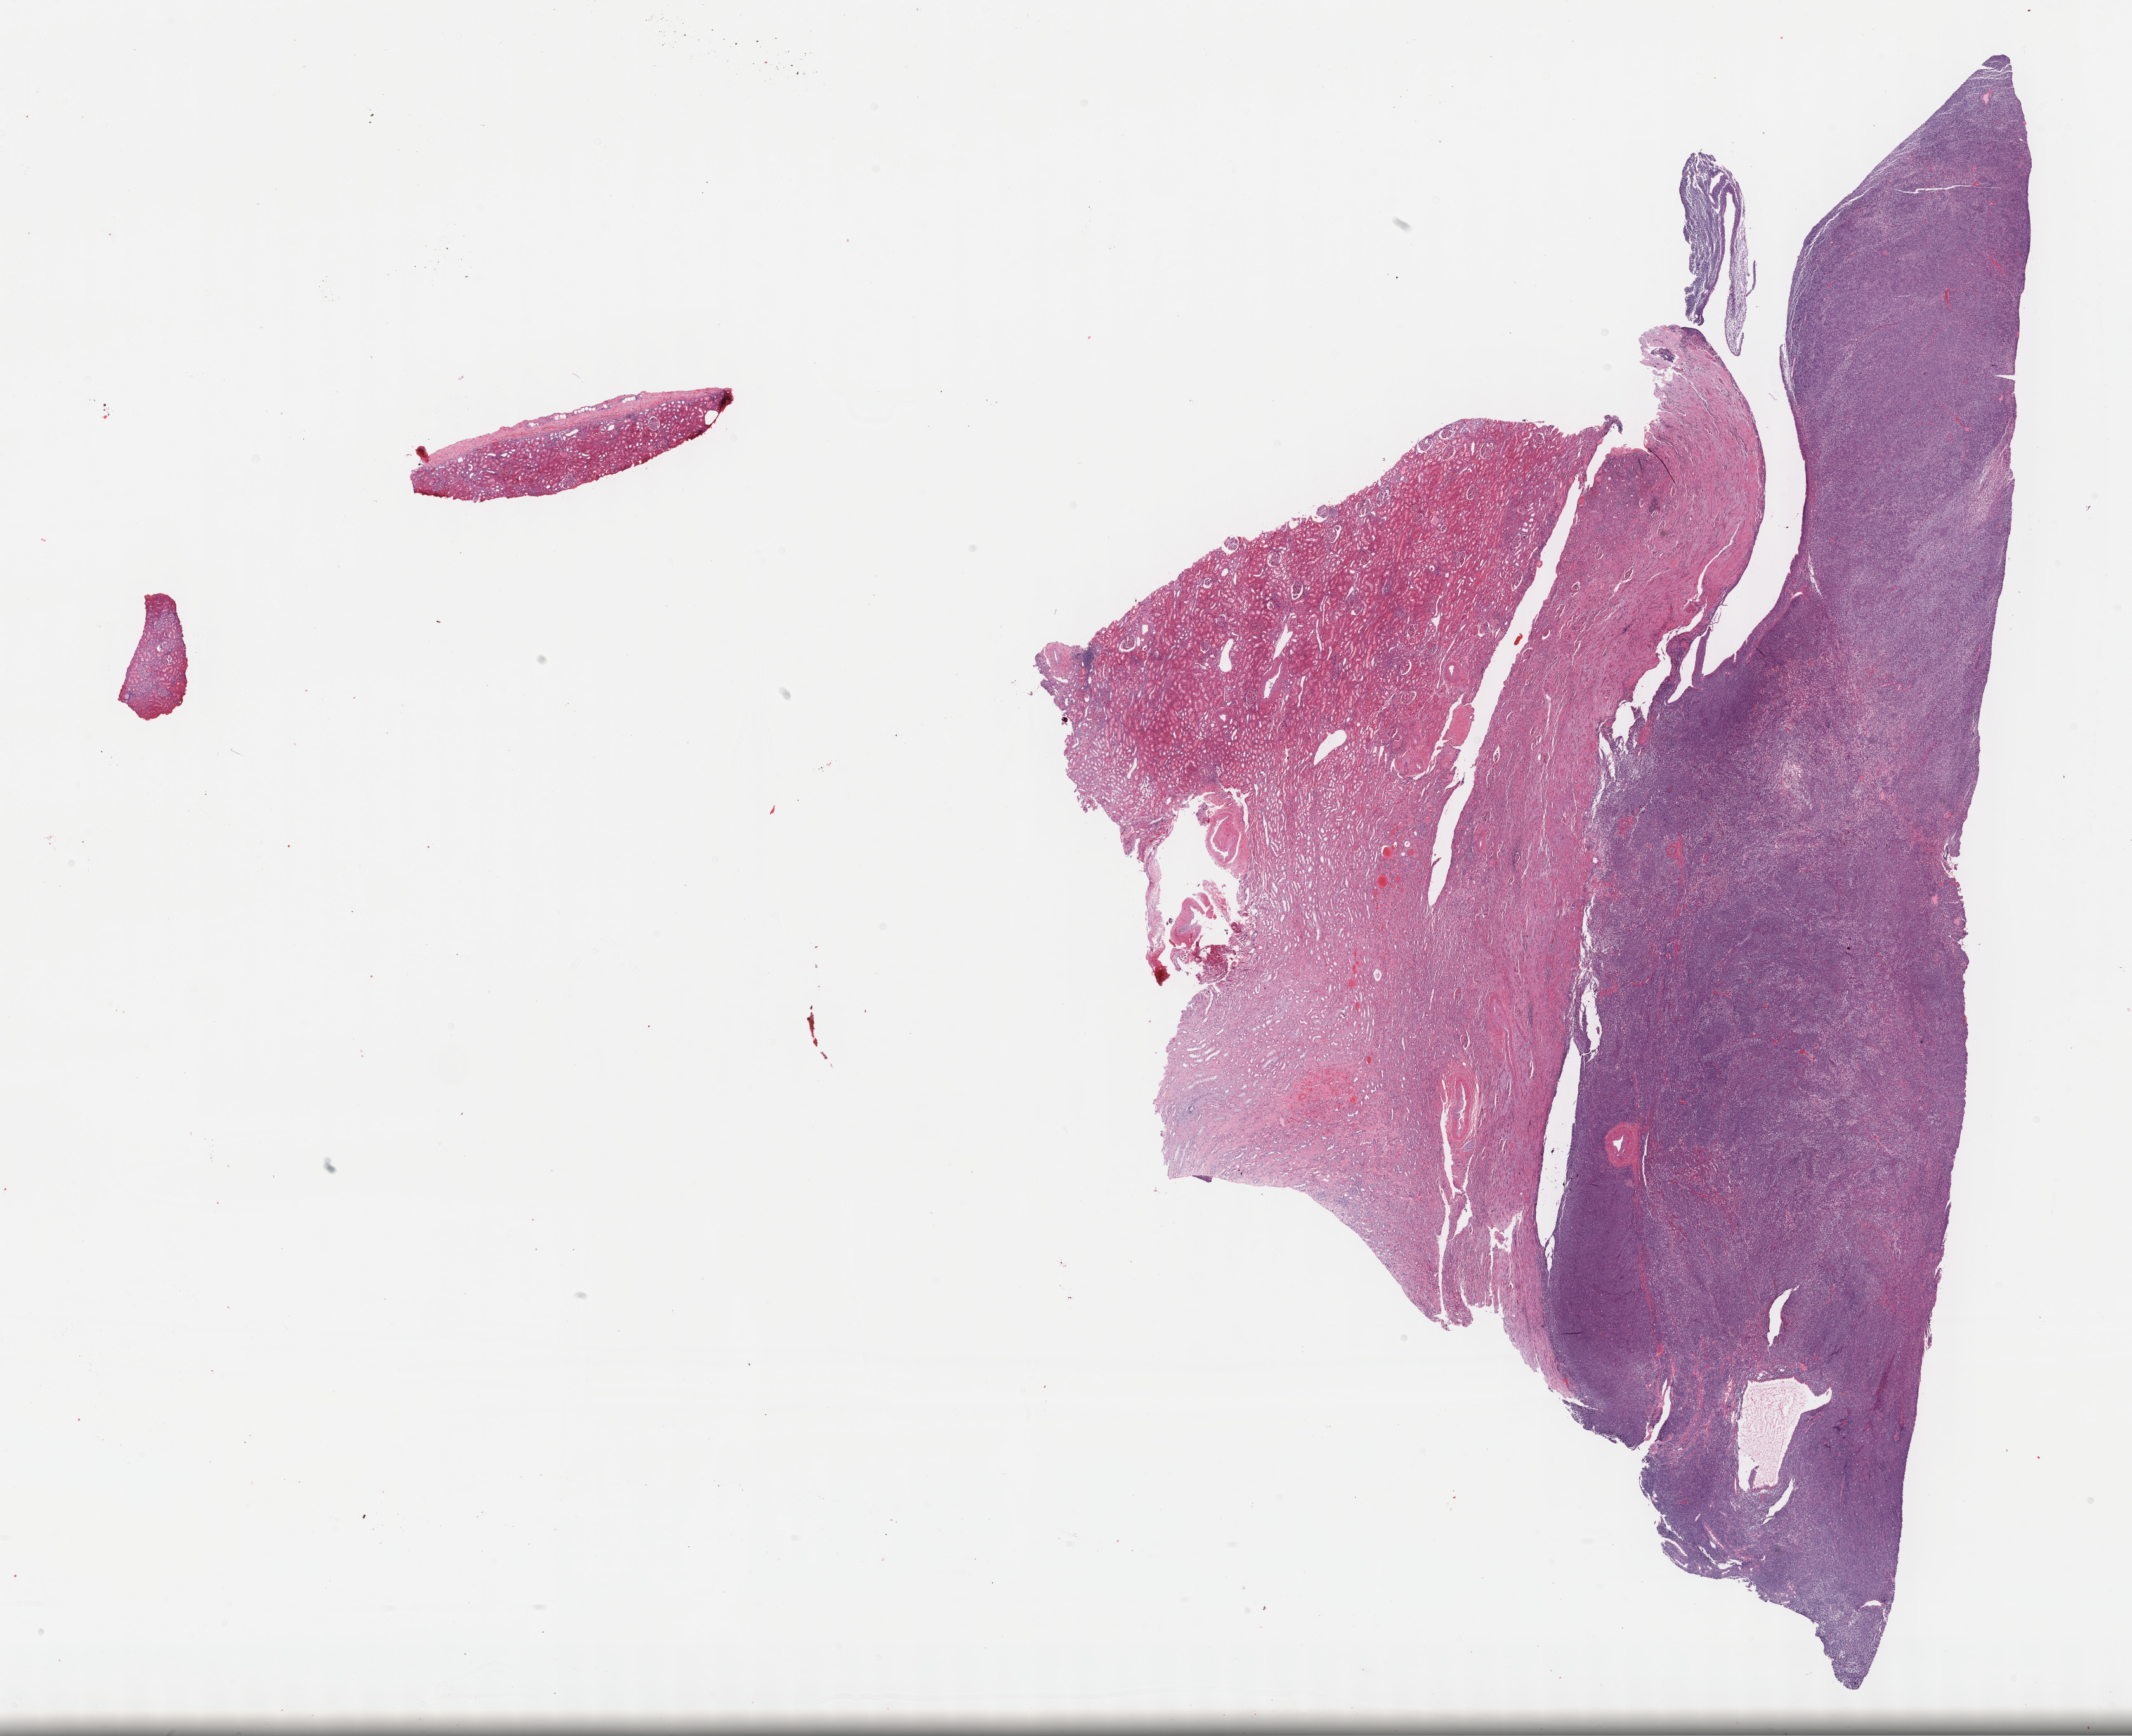
Digitized Hematoxylin and eosin (H&E) stained tissue section (whole slide) — whole scanned area (about 27.2 x 22.1 mm, acquisition: 40x scan) shown as a low-resolution overview. FFPE section. Primary tumour sample from the kidney. Patient: female, age at initial diagnosis 40 years.
Pathologic diagnosis: Synovial sarcoma, spindle cell.